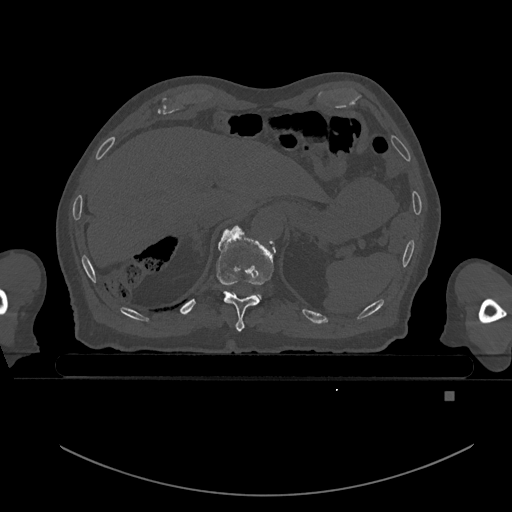
CT including the spine, one axial slice; position 78 of 969 along the scan axis; bone window (W 1800 / L 400 HU); 0.5 mm slice thickness; 512 × 512 image matrix. Male patient, age 82 years. From the clinical record (not read from this slice): primary cancer: prostate.
Structures marked on this image (semi-automatic segmentation, software-assisted and operator-edited):
- T10 vertebra: bounding box (x1, y1, x2, y2) in pixels: (216, 226, 275, 331)
- T11 vertebra: (254, 294, 259, 297)